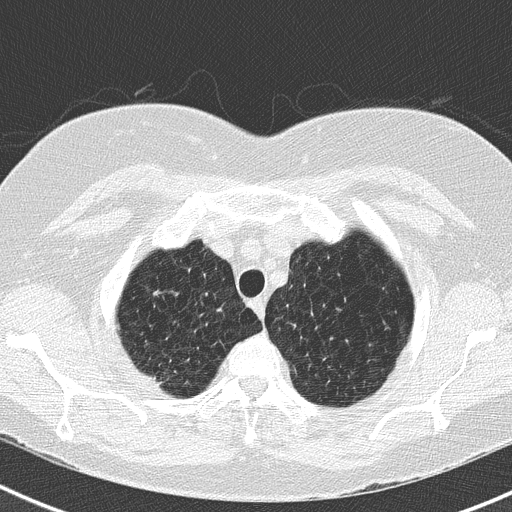
Low-dose screening chest CT, axial slice, second annual screen, lung window (W 1500 / L -600 HU), slice 32 of 183 in the series. Female, age 73 years at enrolment.
Expert-annotated lung lesion, bounding box <129,273,192,322> (left, top, right, bottom; pixels). The screening reader recorded 2 non-calcified nodules or masses ≥4 mm on this exam (right upper lobe, right upper lobe); which of them this box marks is not recorded. Official screen result: positive, no significant change: stable abnormalities potentially related to lung cancer, unchanged since the prior screening exam. Participant outcome: lung cancer diagnosed 250 days after this screen — adenocarcinoma, NOS, right upper lobe, moderately differentiated (G2), stage IB (AJCC 6th edition), 15 mm at pathology.